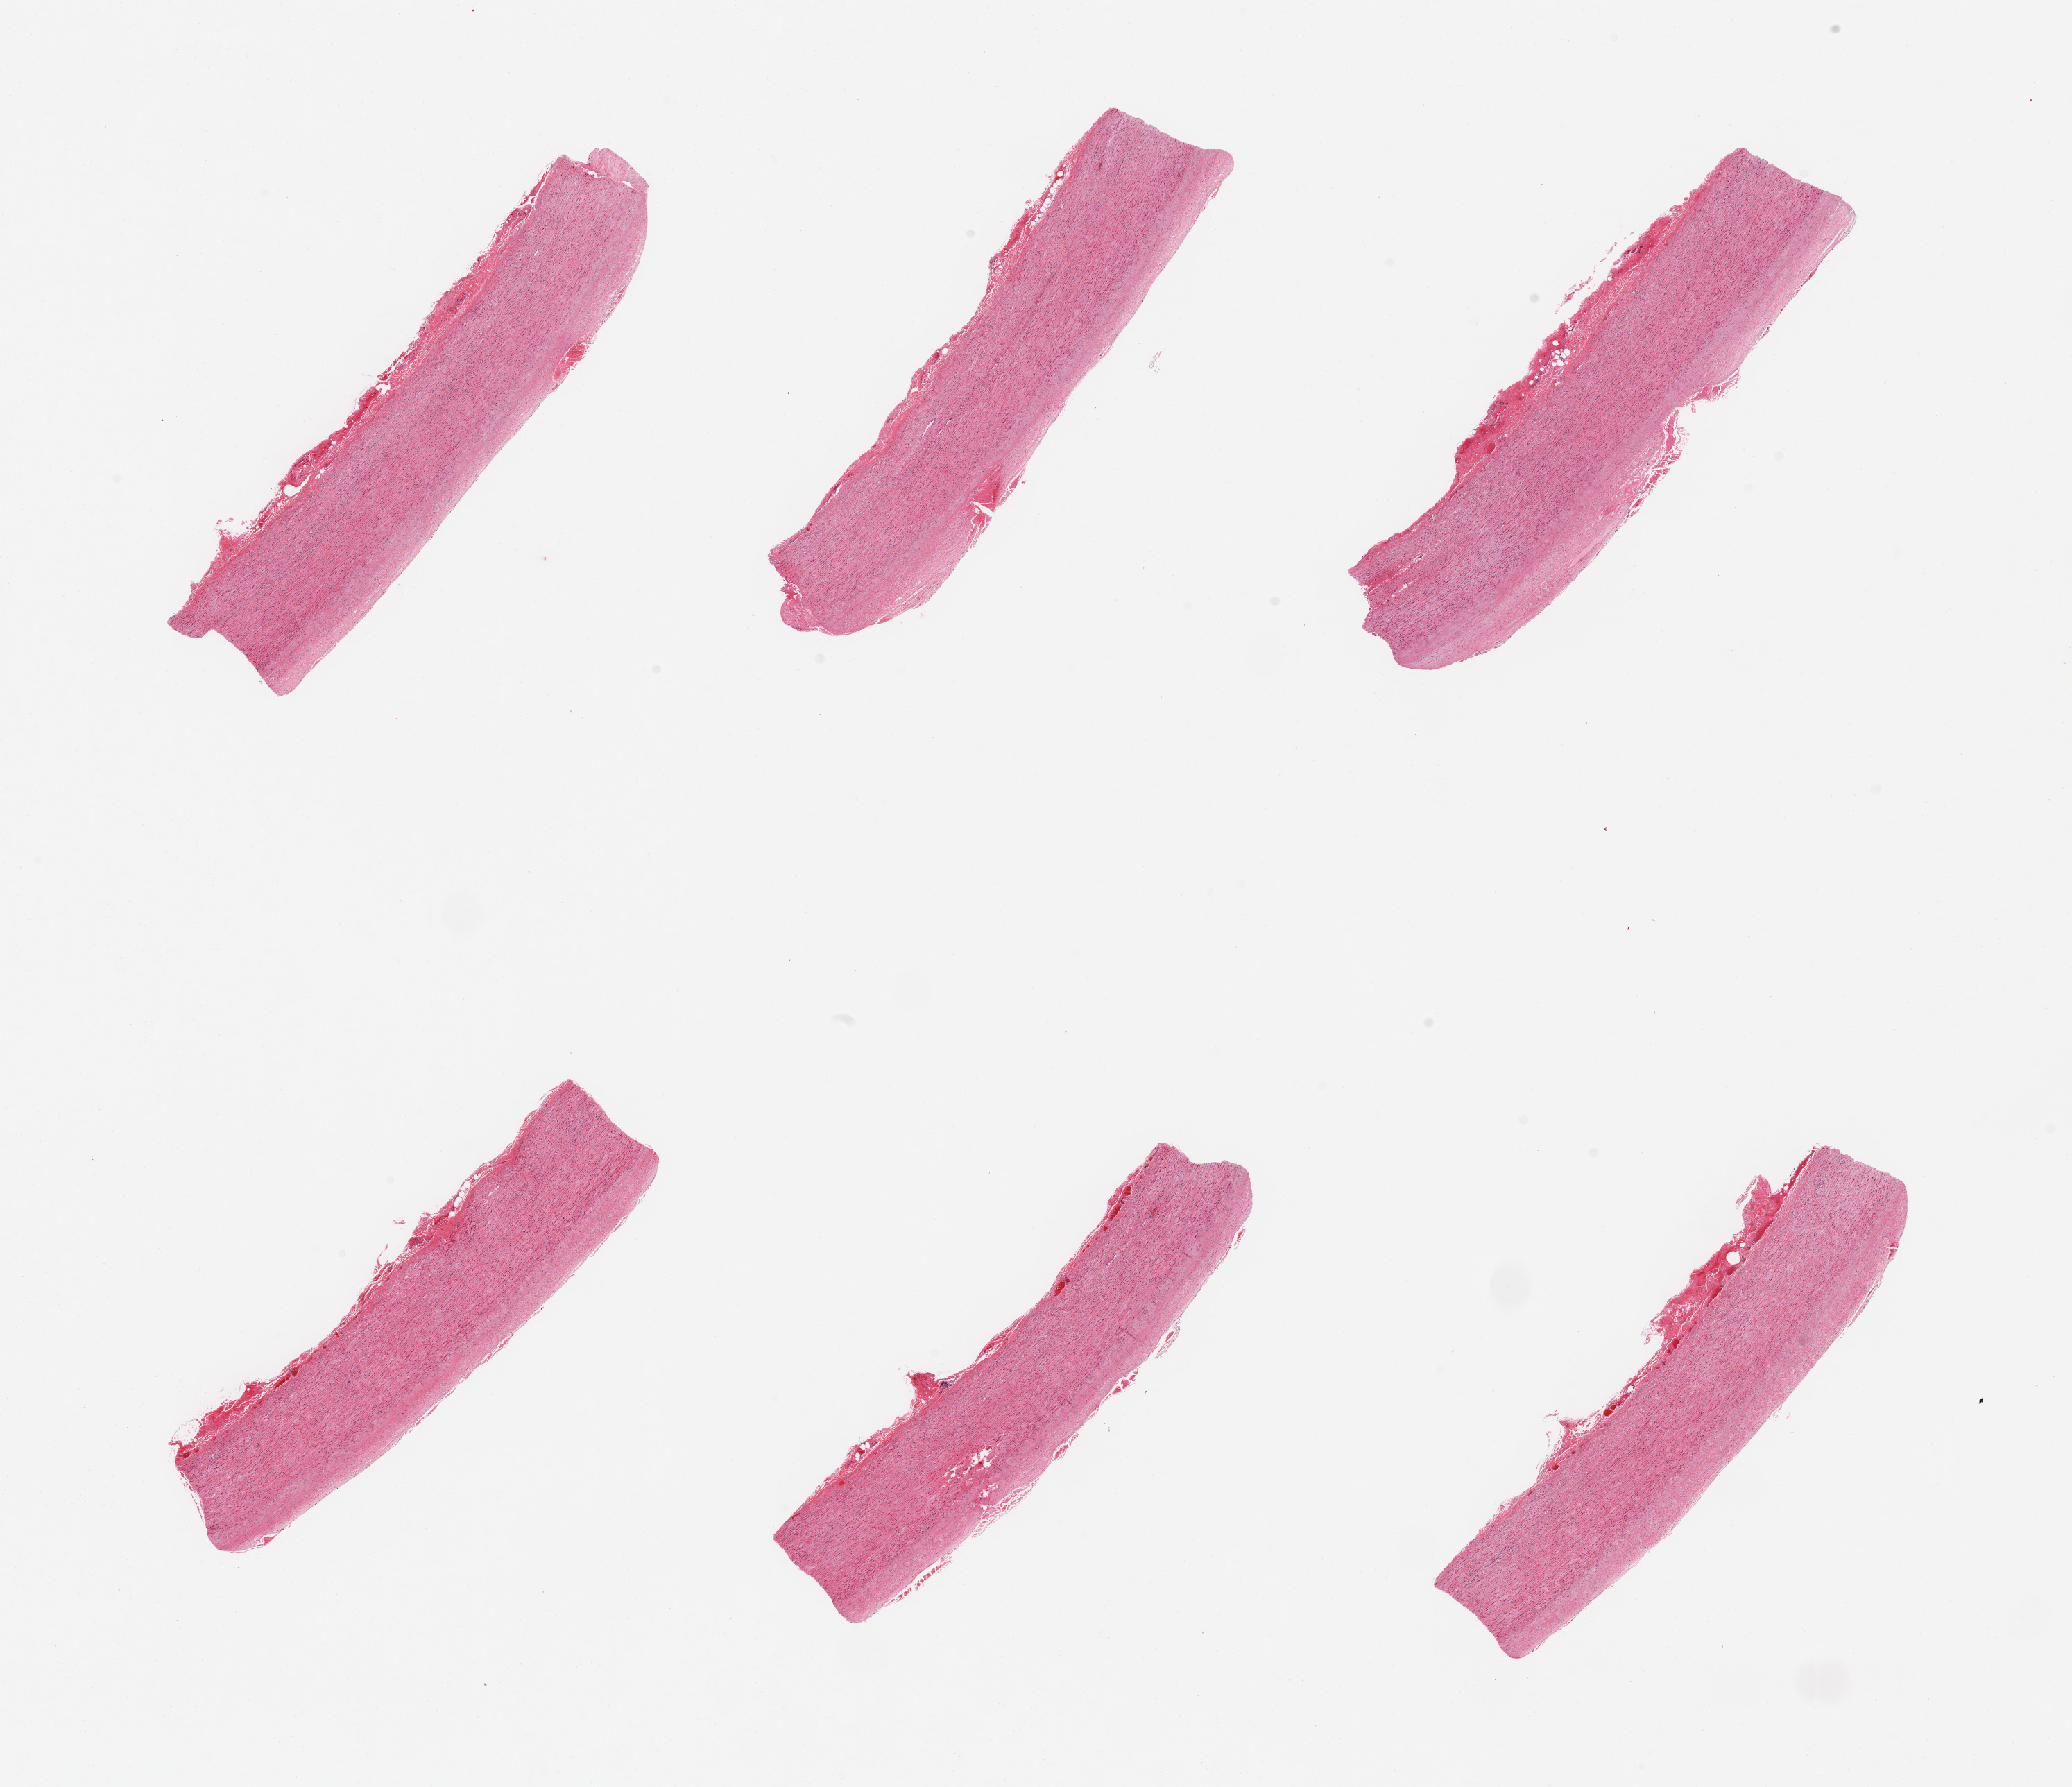
Digitized hematoxylin and eosin (H&E)-stained section, brightfield — whole scanned area (about 23.6 x 20.4 mm) shown as a low-resolution overview; PAXgene-fixed, paraffin-embedded tissue; sampled site (target tissue): aorta; donor tissue sample. Donor sex: male.
Pathologist's review note for this sample: 6 pieces; fibrosclerotic plaque.